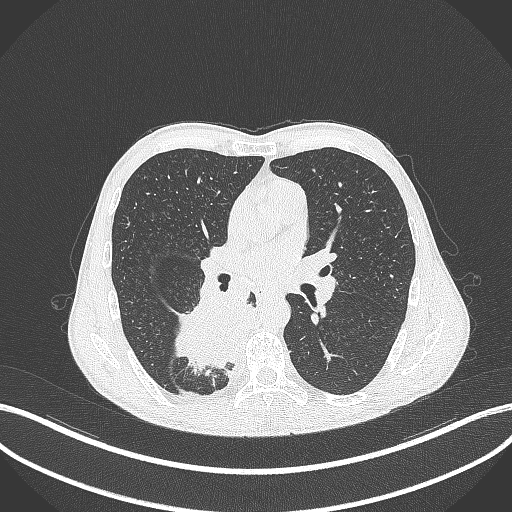
Chest CT, one axial slice; slice 202 of 371 in the series (ordered by position); reconstruction kernel B70f; 120 kVp; lung window (W 1500 / L -600 HU); 512 × 512 image matrix, field of view 400 × 400 mm. Male patient, age 58 years. Case-level facts recorded for this patient, not image findings: clinical TNM (as recorded): T3 N1 M1.
Annotated regions visible in this slice (rectangle marked by the reading radiologist):
- lung tumour (recorded histology: squamous cell carcinoma): bounding box [x1, y1, x2, y2] px = [166, 288, 253, 376]